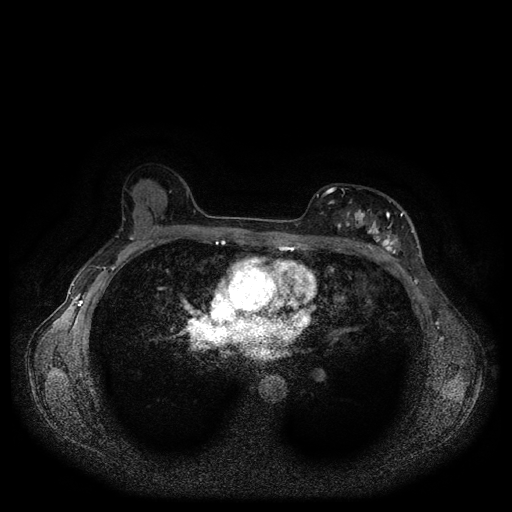
Breast MRI (dynamic contrast-enhanced, multi-phase), one axial slice. Position 64 of 116 along the scan axis. Dynamic contrast-enhanced series, time point 2 of 5 at this slice position (early post-contrast). 1.5 T. TE 2.6 ms, TR 5.3 ms. 2 mm slice thickness. 512 × 512 image matrix, field of view 350 × 350 mm. Patient: female, 51 years.
Outlined on this slice (semi-automatic segmentation, software-assisted and operator-edited):
- breast lesion (labelled 'tumour' in the annotation; benign lesions carry a separate 'benign' label): bounding box <331,206,403,256> (left, top, right, bottom; pixels)